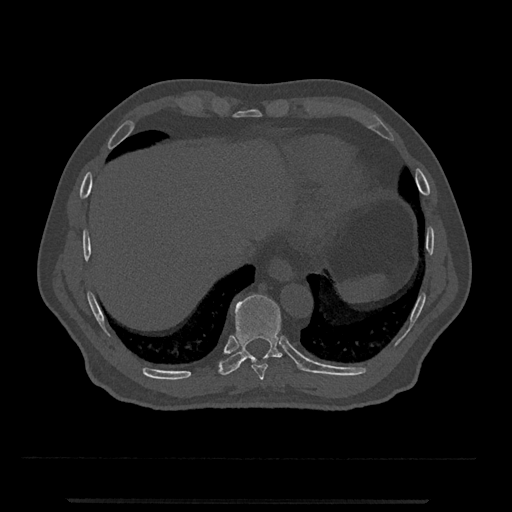
CT including the spine, one axial slice; 120 kVp; bone window (W 1800 / L 400 HU); 0.5 mm slice thickness; 512 × 512 image matrix. Male patient, age 63 years. From the clinical record (not read from this slice): primary cancer: prostate.
Structures marked on this image (semi-automatically segmented with operator editing):
- T10 vertebra: box from (x=218, y=294) to (x=283, y=375) px
- T9 vertebra: (x=251, y=364)–(x=268, y=380)